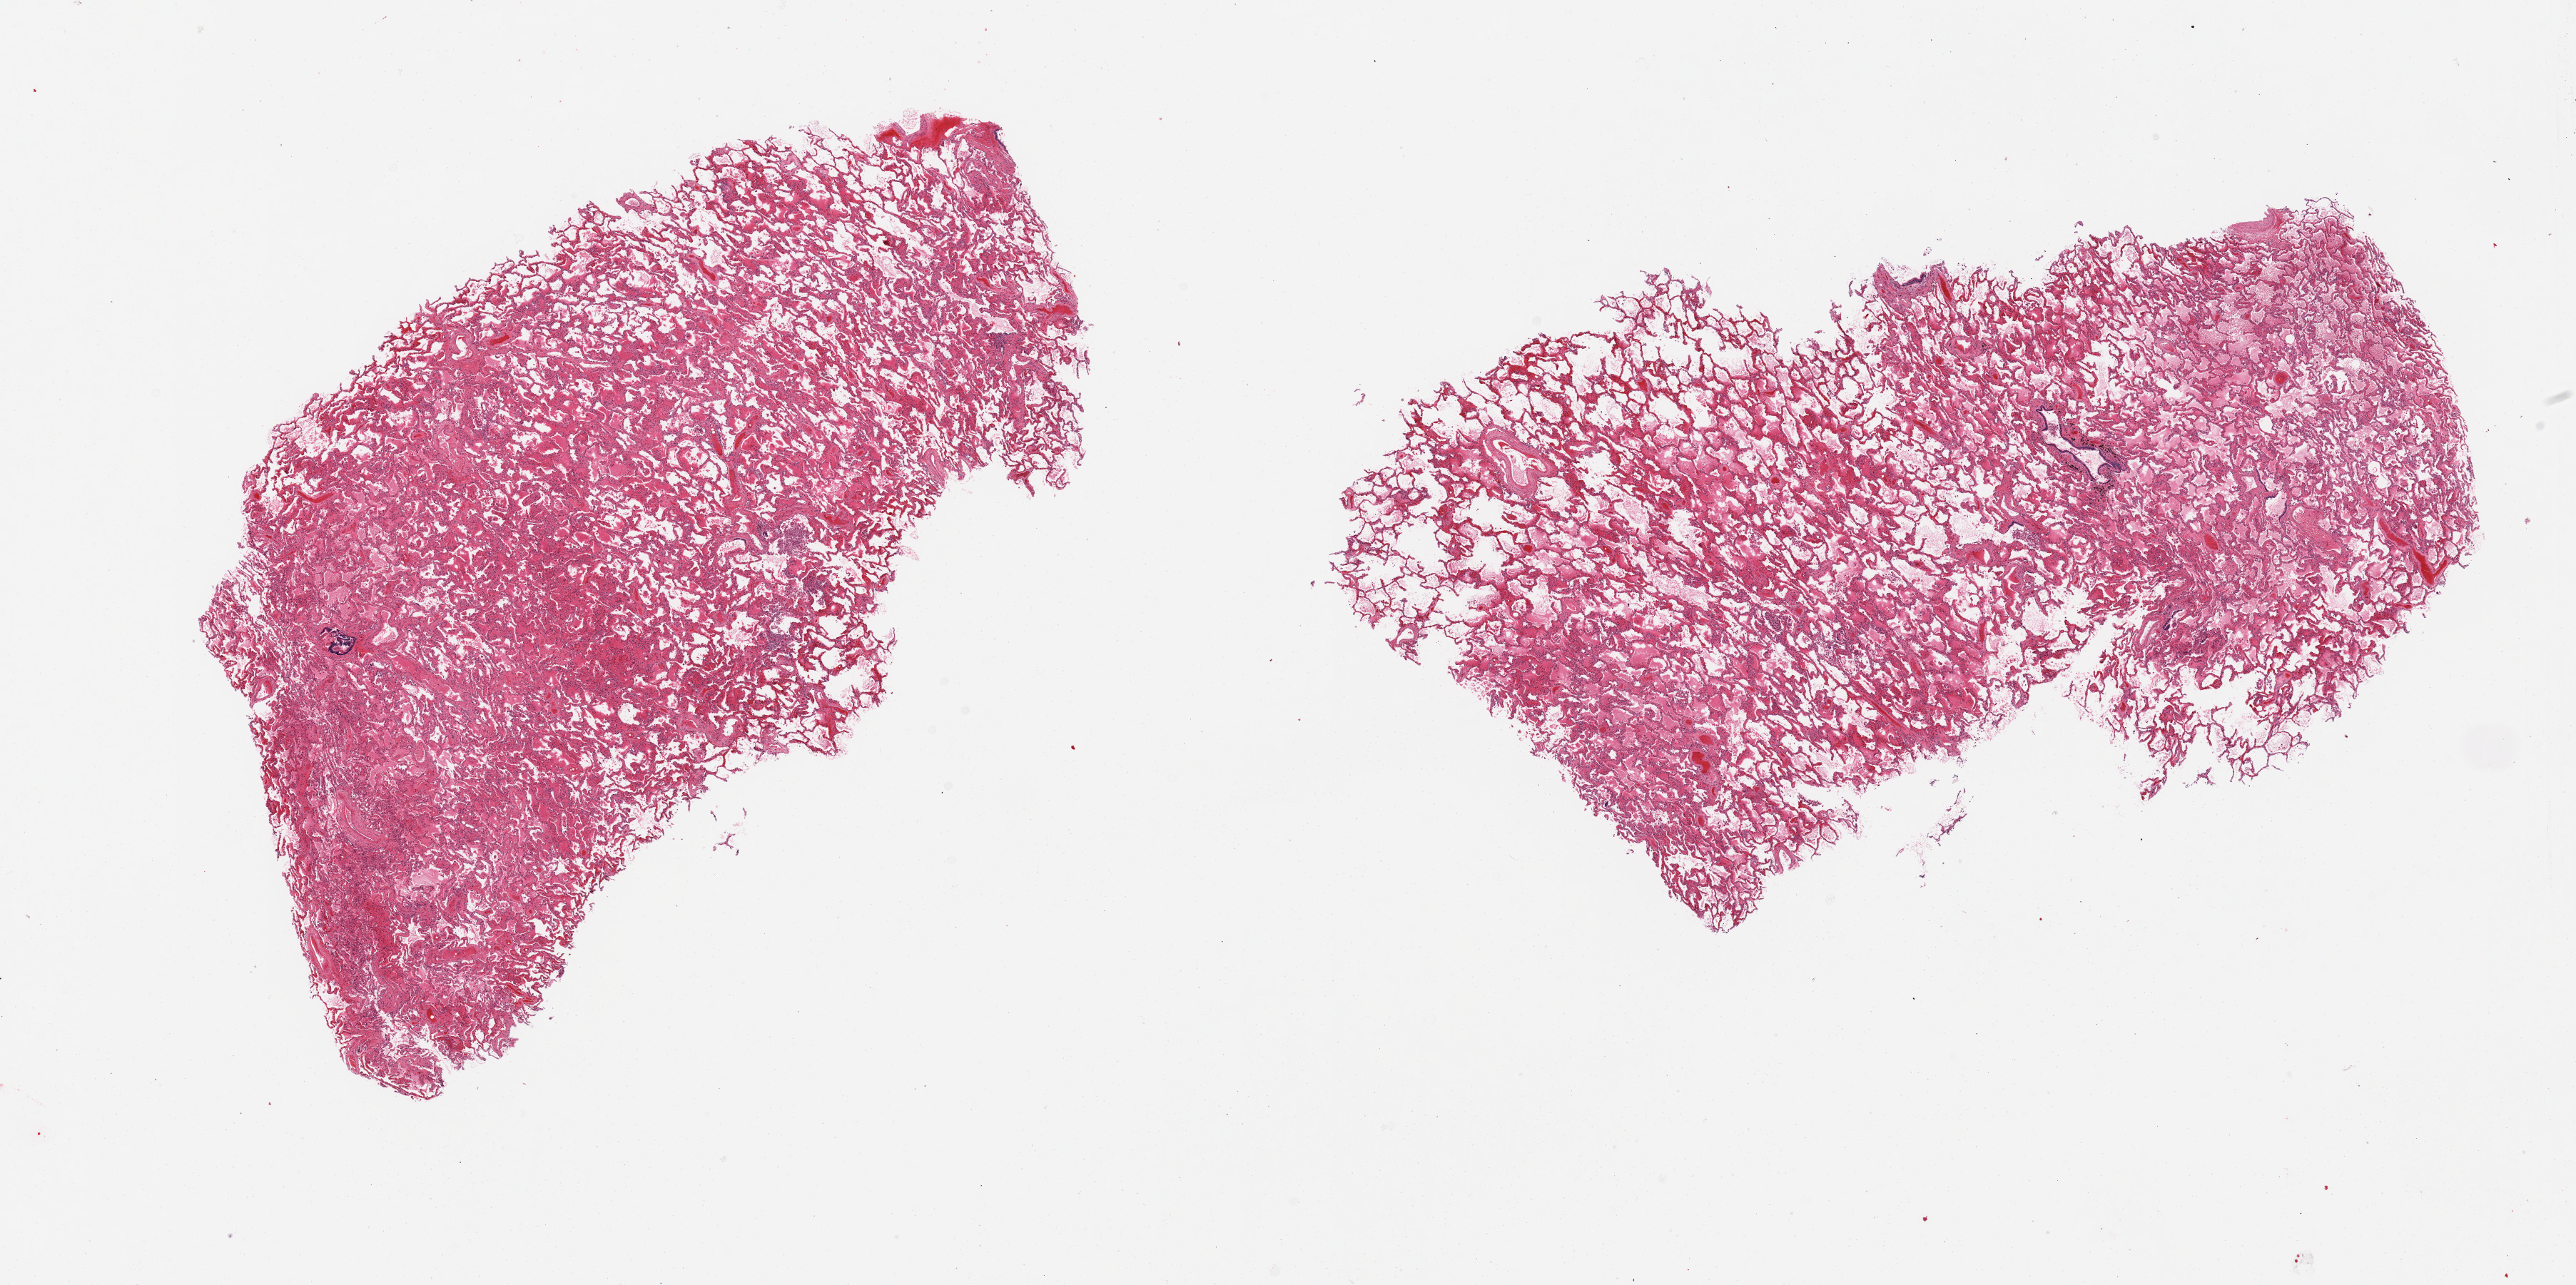
Digitized haematoxylin and eosin-stained section, brightfield, low-resolution overview of the scanned area, about 28.5 x 14.2 mm. PAXgene-fixed, paraffin-embedded tissue. Target tissue: lung. Donor tissue sample. Donor: female.
• review note (as recorded): 2 pieces; acute and chronic vascular congestion; pulmonary edema